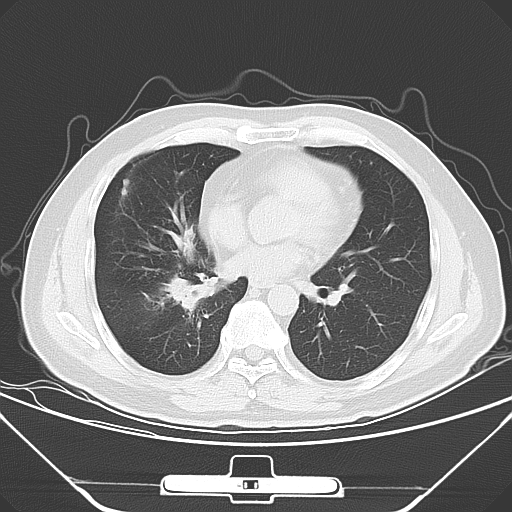
Chest CT, one axial slice. Position 25 of 56 along the scan axis. 120 kVp. Lung window (W 1500 / L -600 HU). 512 × 512 image matrix. Patient: male, 48 years. Case-level facts recorded for this patient, not image findings: clinical TNM (as recorded): T1a N1 M1c; histopathological grade: G3.
Structures marked on this image (rectangle marked by the reading radiologist):
- lung tumour (recorded histology: adenocarcinoma): bounding box [x1, y1, x2, y2] px = [158, 268, 222, 312]